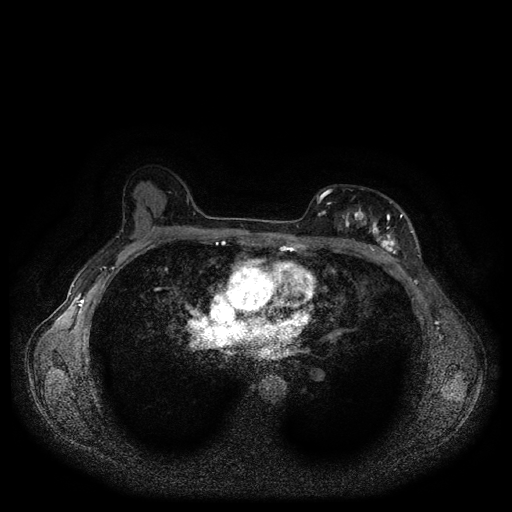
Breast MRI (dynamic contrast-enhanced, multi-phase), one axial slice. Dynamic contrast-enhanced series, time point 2 of 5 at this slice position (early post-contrast). 1.5 T. TE 2.6 ms, TR 5.3 ms. 2 mm slice thickness. 512 × 512 image matrix, field of view 350 × 350 mm. Female patient, age 51 years.
Structures marked on this image (semi-automatically segmented with operator editing):
- breast lesion (labelled 'tumour' in the annotation; benign lesions carry a separate 'benign' label): bounding box <329,206,401,260> (left, top, right, bottom; pixels)